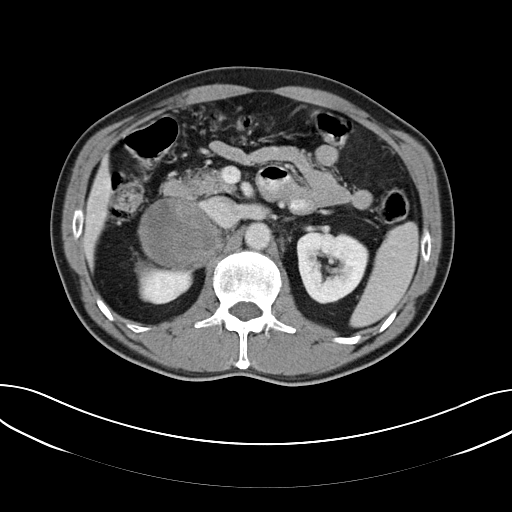
Contrast-enhanced abdominal CT, one axial slice. Slice 31 of 61 in the series (ordered by position). Intravenous contrast given. Soft-tissue window (W 400 / L 40 HU). 512 × 512 image matrix. Patient: male, 57 years. Case-level facts recorded for this patient, not image findings: diagnosis: adrenocortical carcinoma; tumour side: right adrenal; tumour size at pathology: 11.2 cm; Ki-67 index: 10 %; stage (as recorded): 3.
Structures marked on this image (semi-automatically segmented with operator editing):
- mass: bounding box <140,199,219,267> (left, top, right, bottom; pixels)